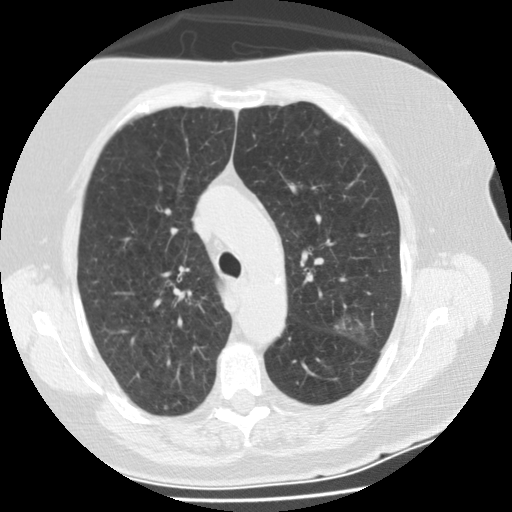
Low-dose screening chest CT, axial slice. Second screening round (one year after baseline). Lung window (W 1500 / L -600 HU). Slice 83 of 297 in the series. Female participant, aged 74 years at enrolment. Former smoker at enrolment.
• Expert reader's lesion annotation, bounding box [x1, y1, x2, y2] px = [326, 304, 387, 359].
• The screening reader recorded 3 non-calcified nodules or masses ≥4 mm on this exam (right lower lobe, left upper lobe, left upper lobe); which of them this box marks is not recorded.
• Later outcome: lung cancer diagnosed 68 days after this screen — bronchiolo-alveolar adenocarcinoma, NOS, left upper lobe, stage IA (AJCC 6th edition), 20 mm at pathology.